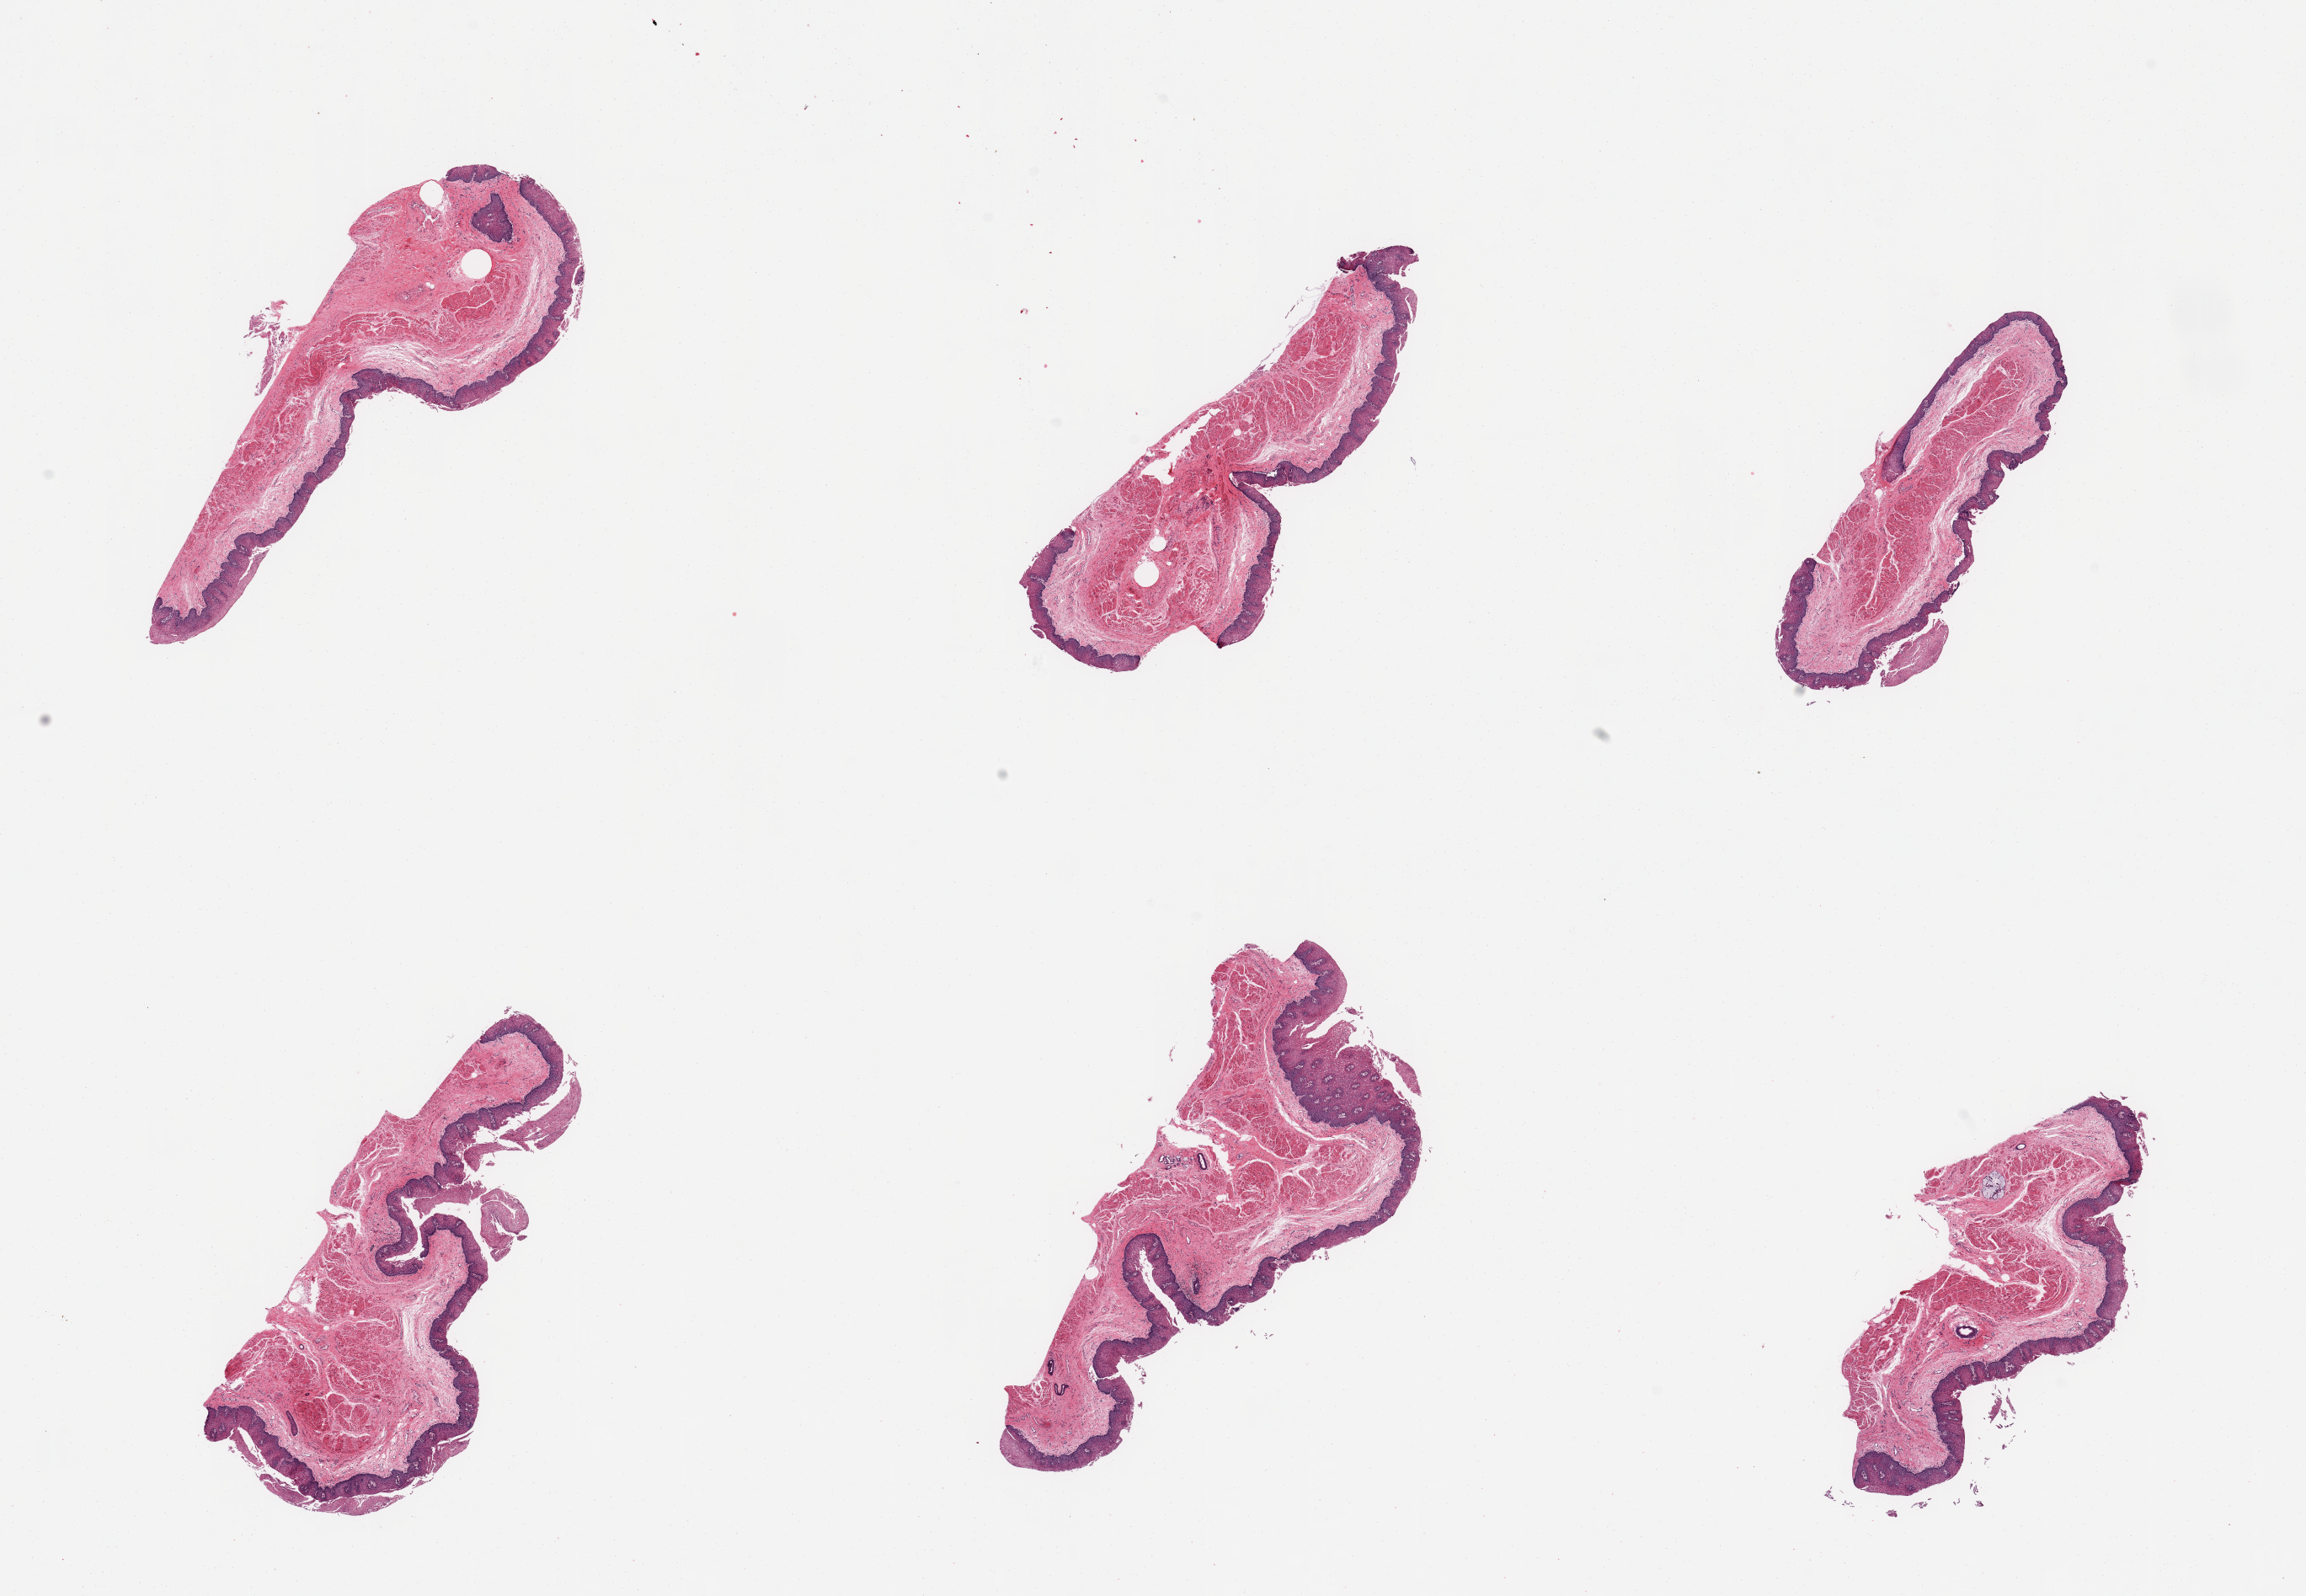
Digitized hematoxylin and eosin (H&E)-stained section, brightfield — whole scanned area (about 21.7 x 15.0 mm) shown as a low-resolution overview. PAXgene-fixed paraffin-embedded (PFPE) section. Target tissue: esophageal mucous membrane. Tissue donor sample. Donor: female.
* review note (as recorded): 6 pieces; well dissected; no submucosa